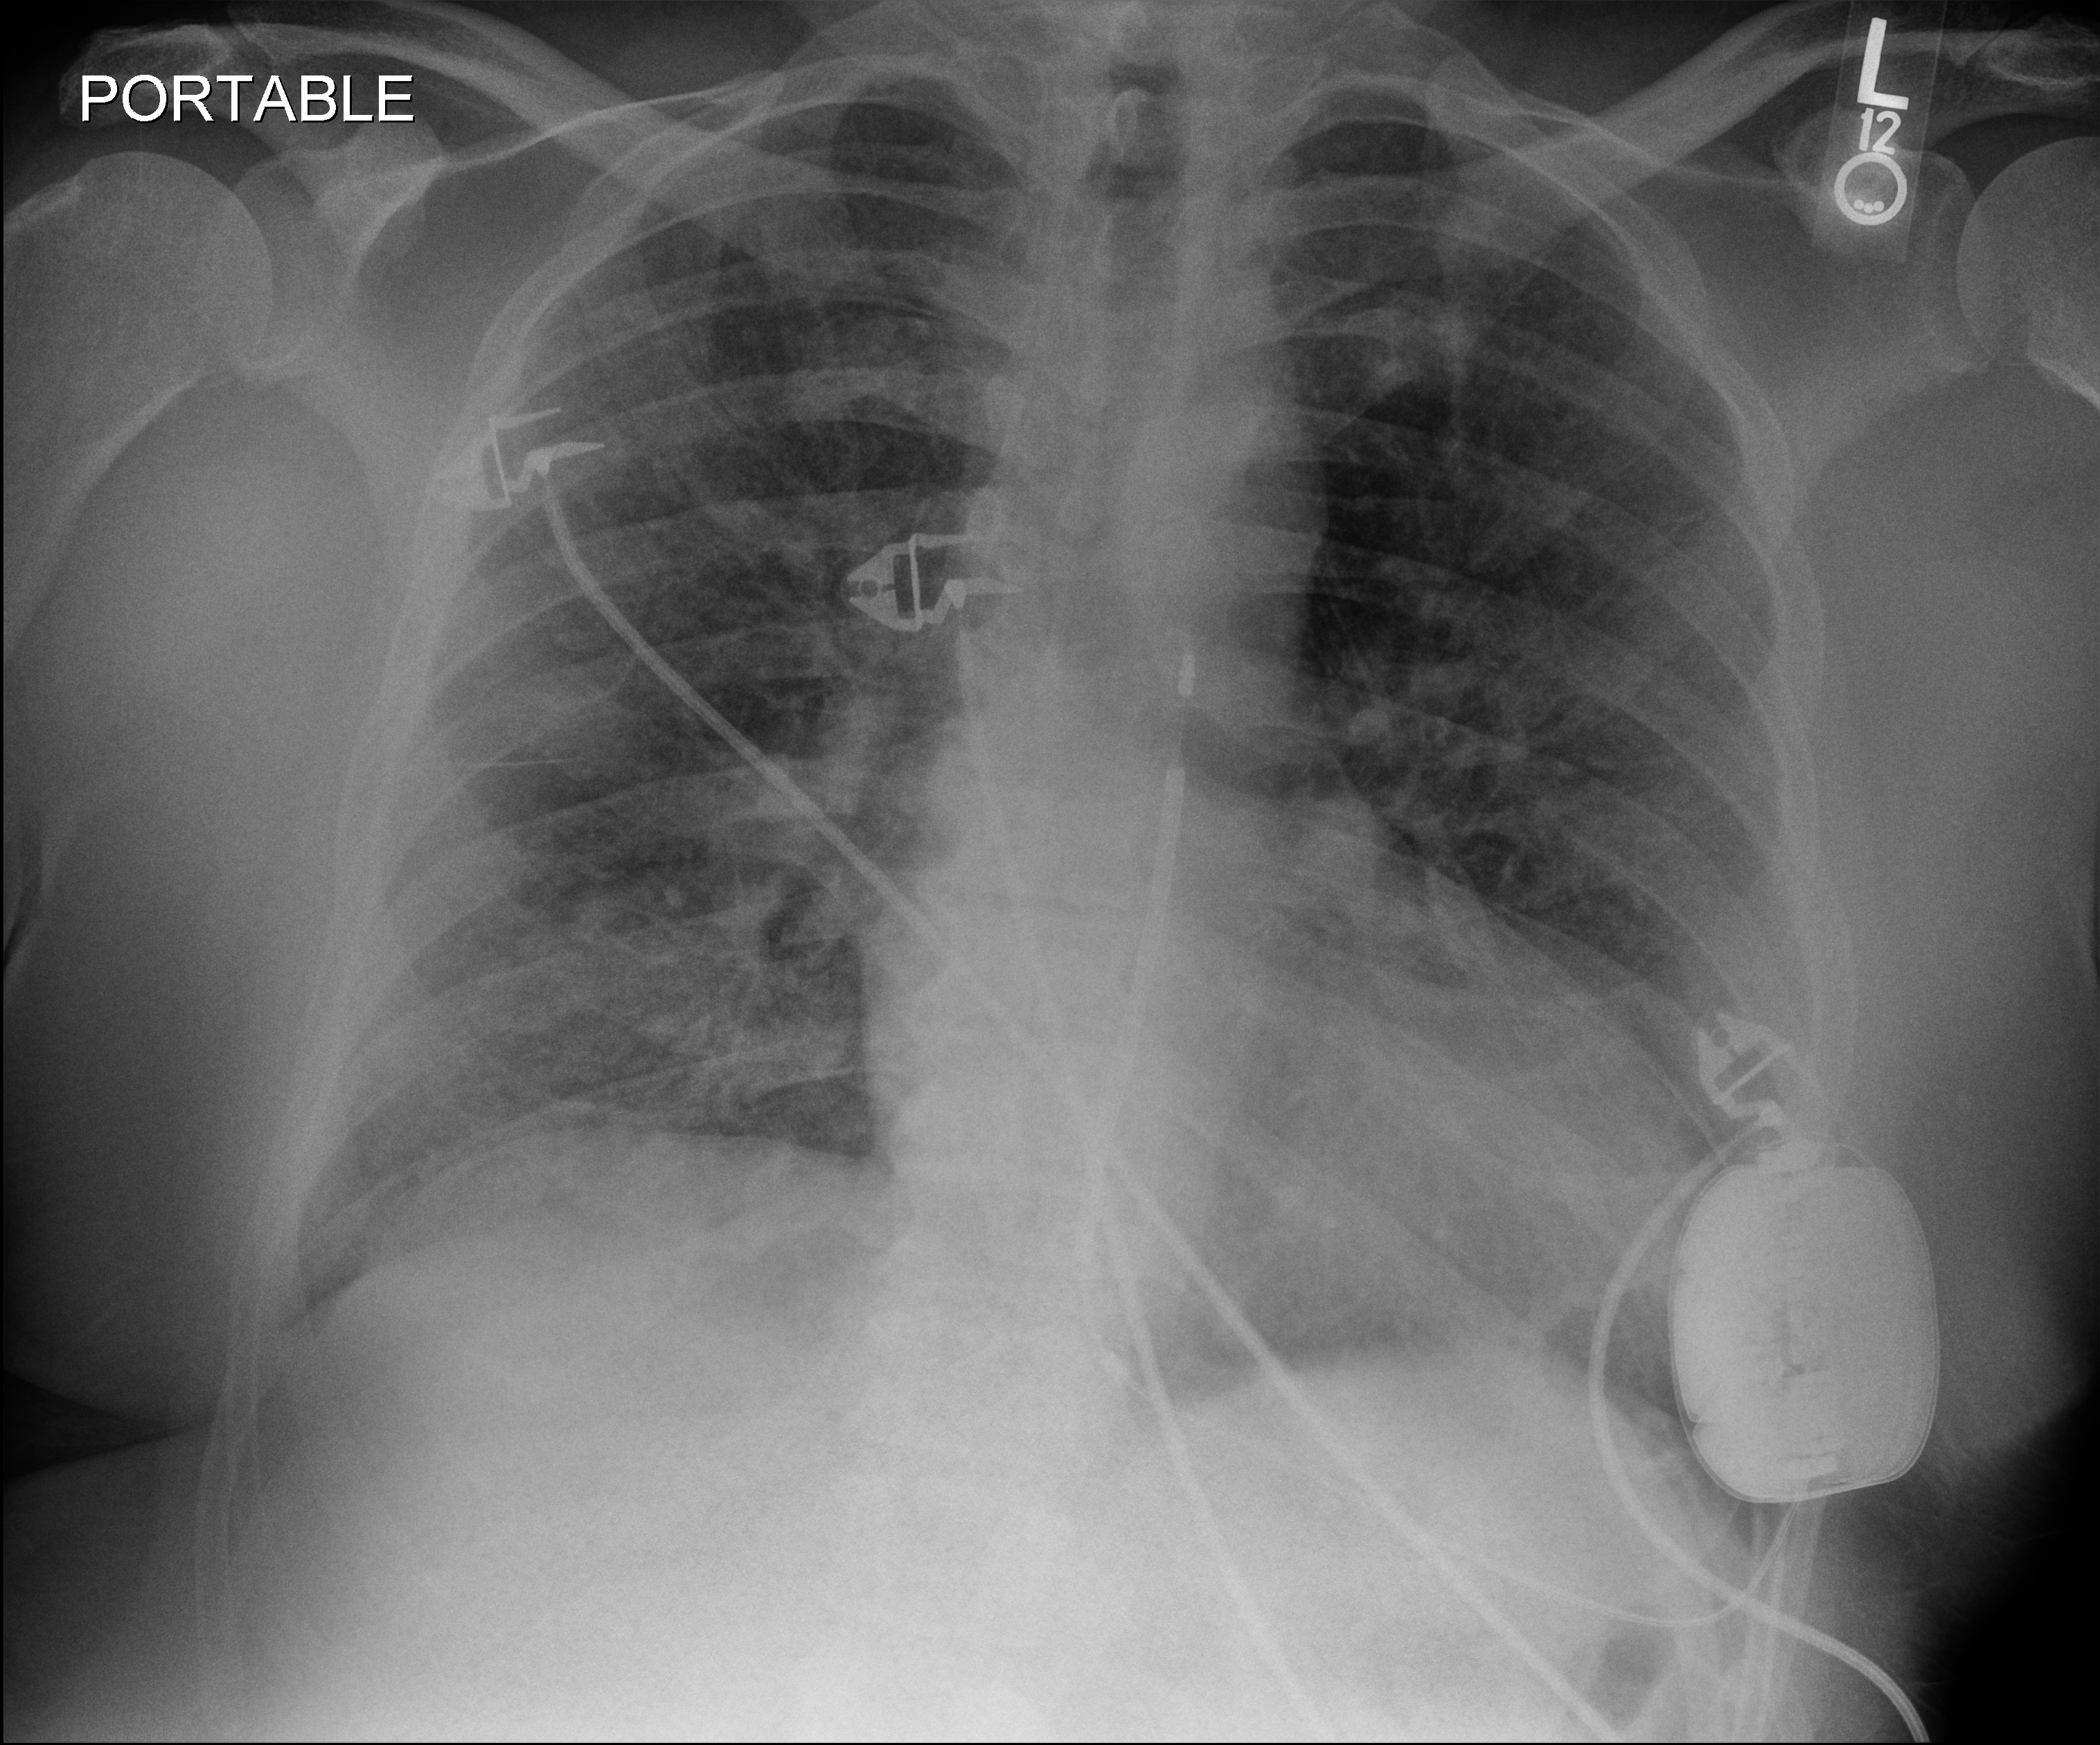
Bedside chest radiograph (digital radiography). Patient hospitalised with COVID-19; male, aged 60–74 years.
Hospital-stay facts (about this admission, not read from this image; timing relative to this image not recorded):
- mechanically ventilated during this hospital stay: yes
- admitted to intensive care during this hospital stay: yes